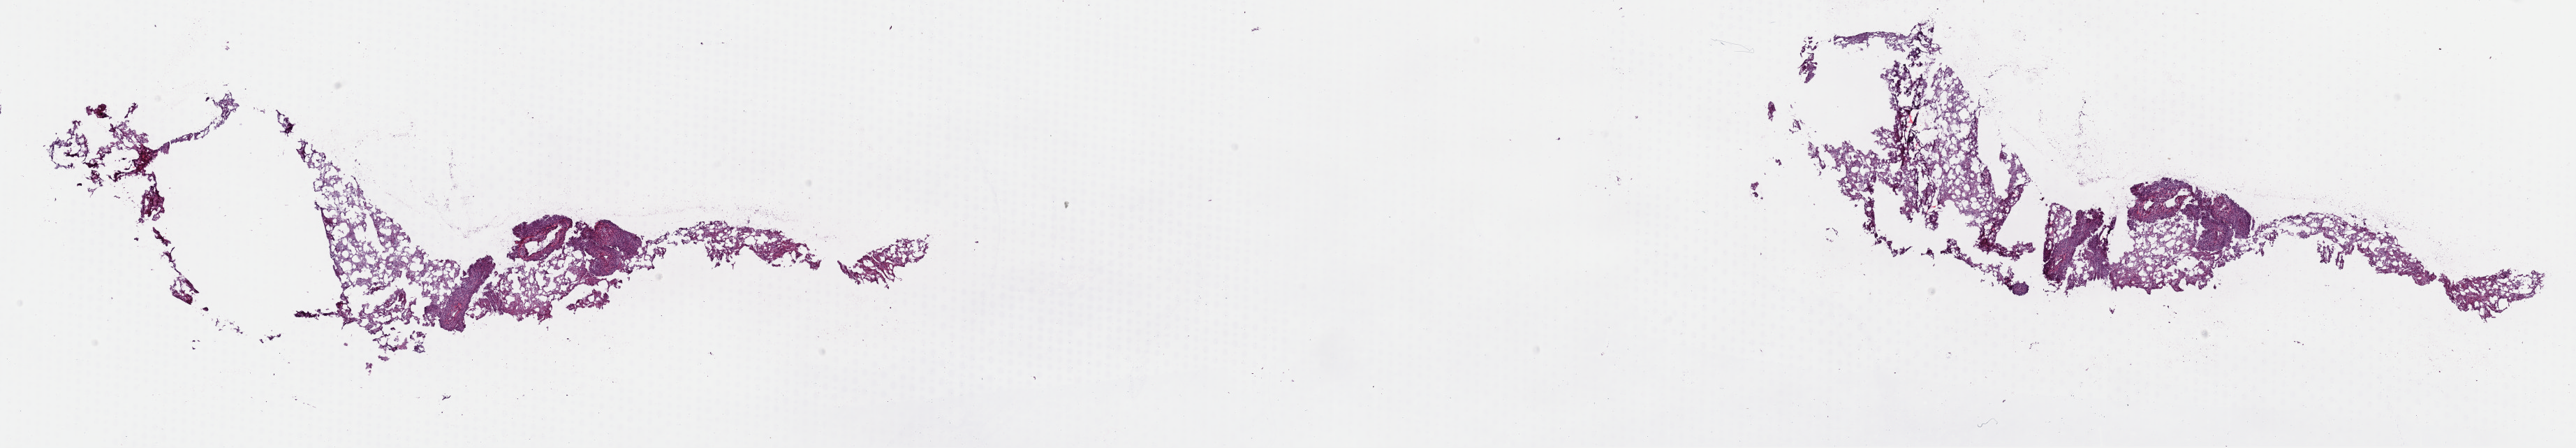
Whole-slide histology image, Hematoxylin and eosin (H&E) stained, low-resolution overview of the scanned area, about 29.1 x 5.1 mm (slide scanned at 40x); frozen section from the top of the tissue portion; primary tumour sample from the retroperitoneum and peritoneum. Female, age 37 years at initial diagnosis. Pathologist review of this section (percent, as recorded): tumour cells 100%, tumour nuclei 85%, normal cells 0%, stromal cells 0%, necrosis 0%. Inflammatory infiltration, as recorded: lymphocyte infiltration 1%, monocyte infiltration 0%, neutrophil infiltration 0%.
Histologic diagnosis: Liposarcoma, well differentiated (retroperitoneum).